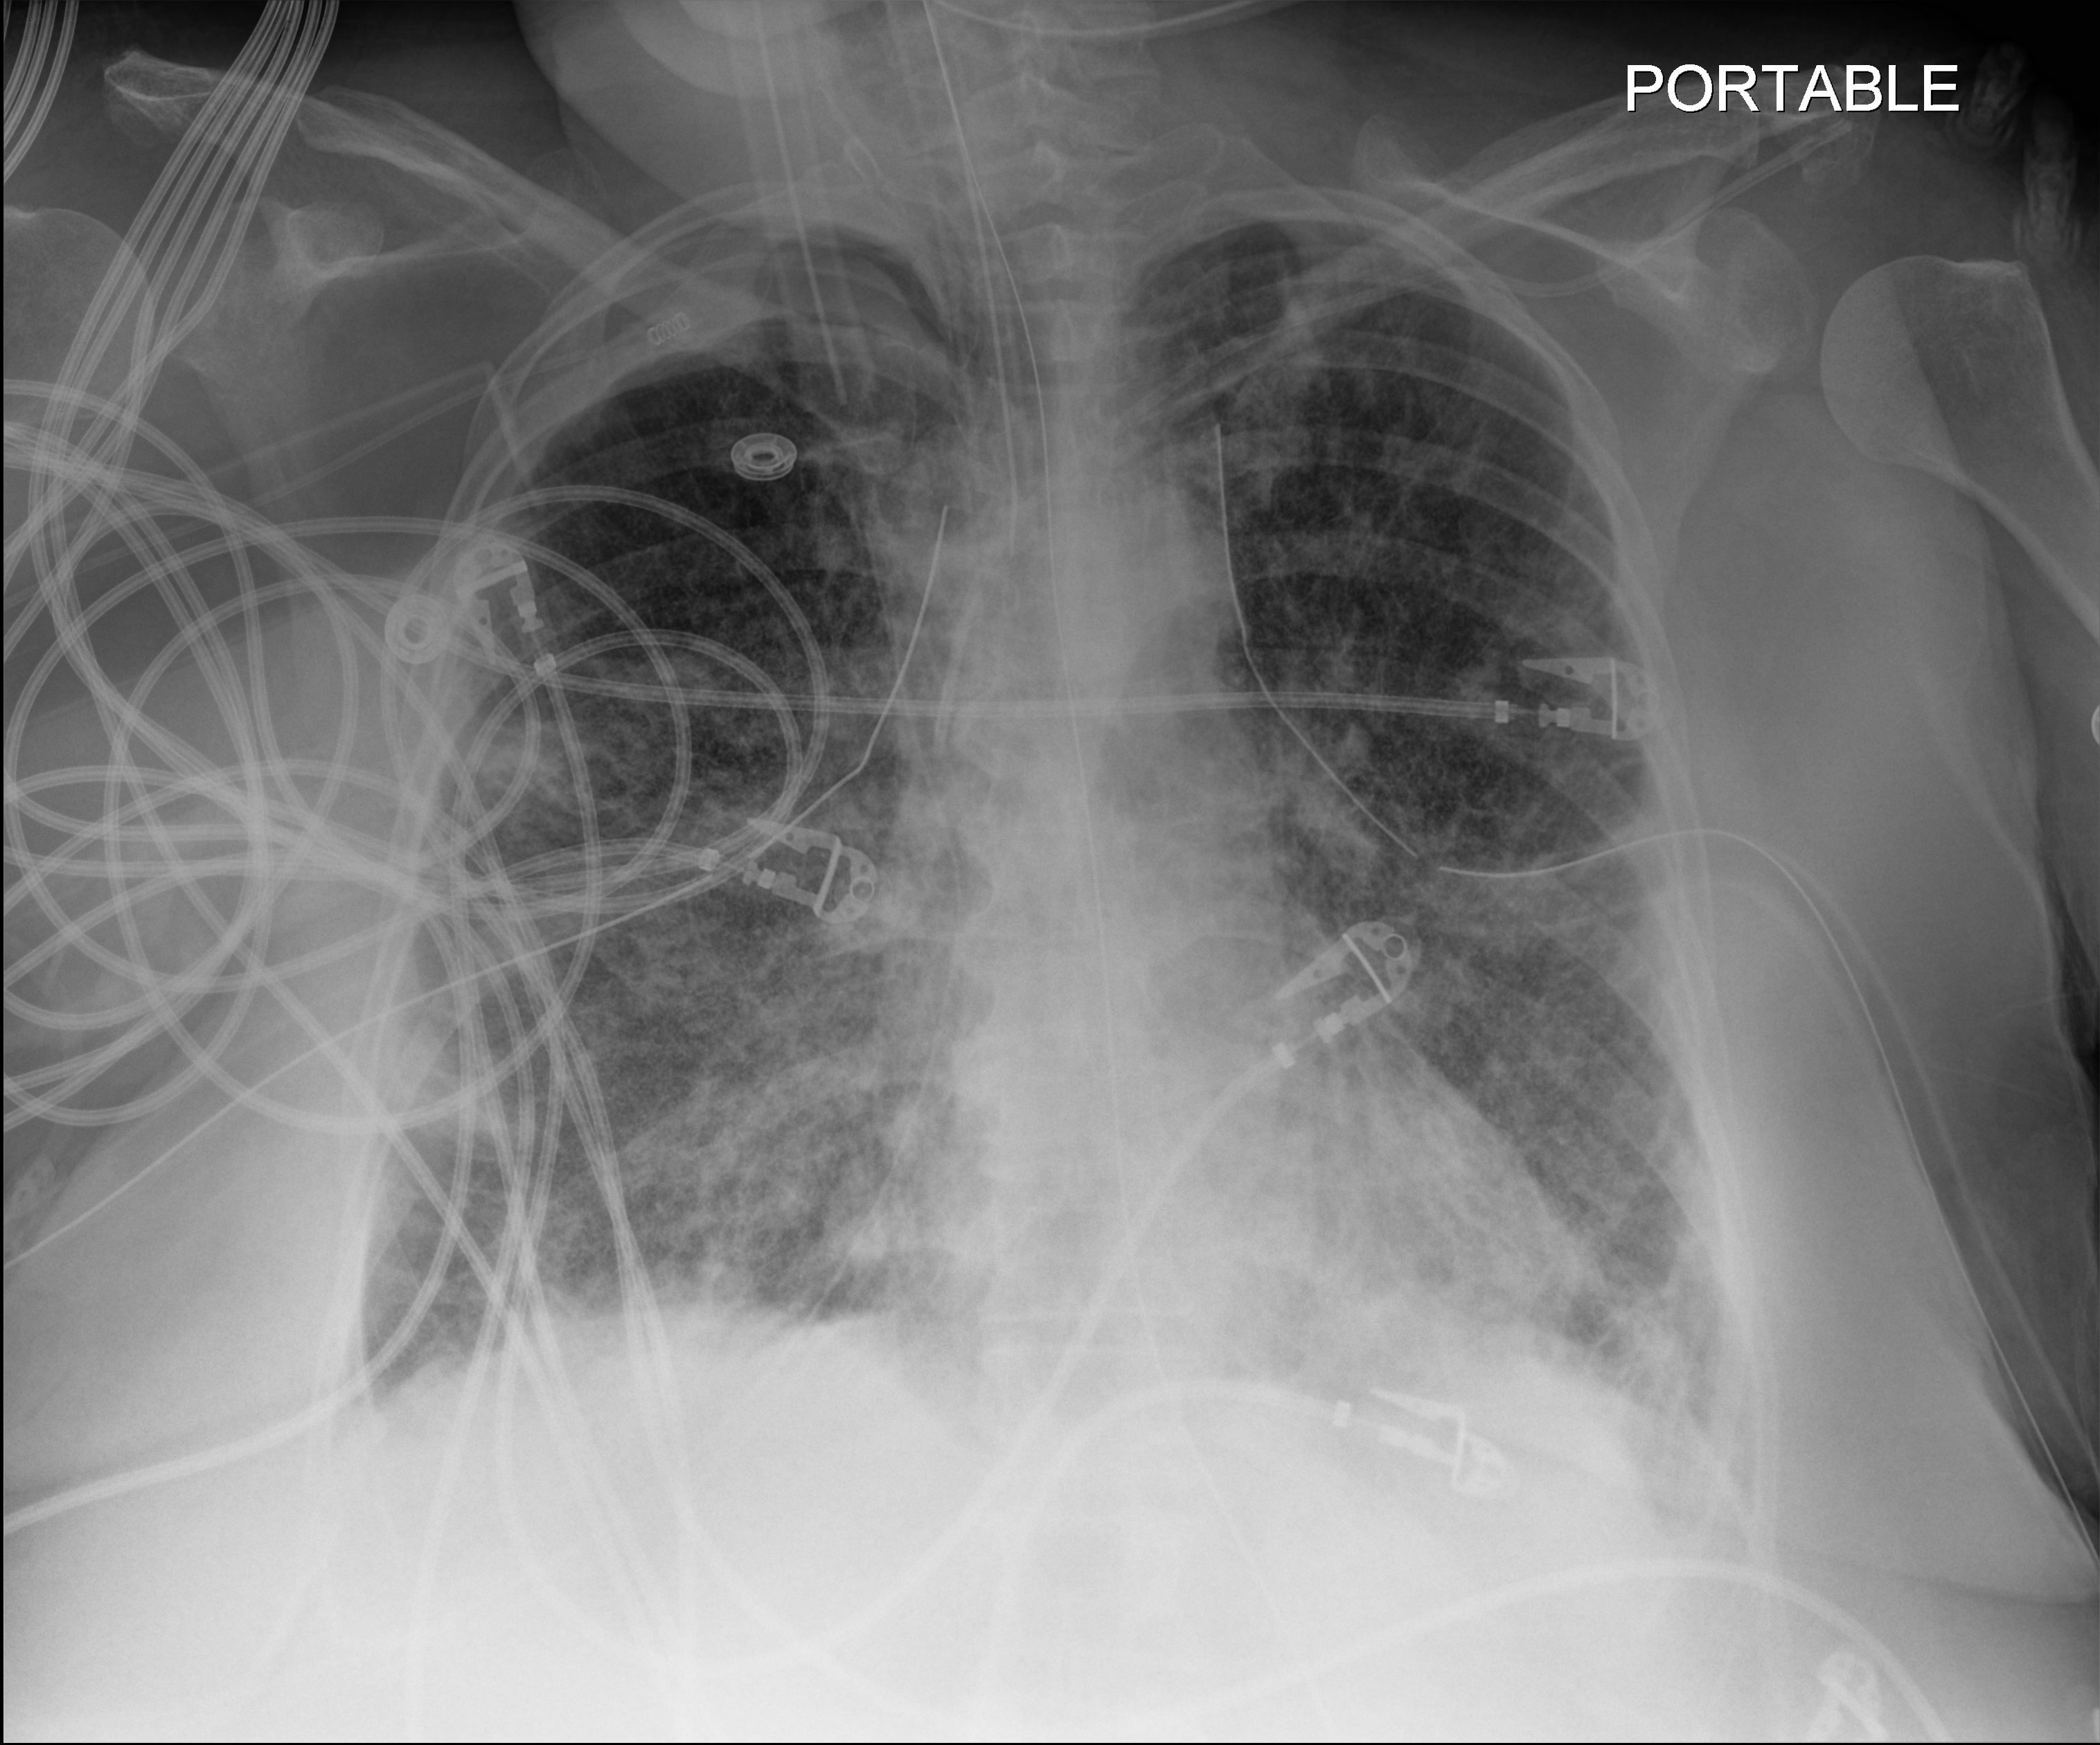
Bedside chest radiograph (digital radiography). Patient hospitalised with COVID-19; female, aged 60–74 years.
From the hospital-stay record, not from the radiograph (when in the stay this image was taken is not recorded):
- admitted to intensive care during this hospital stay: yes